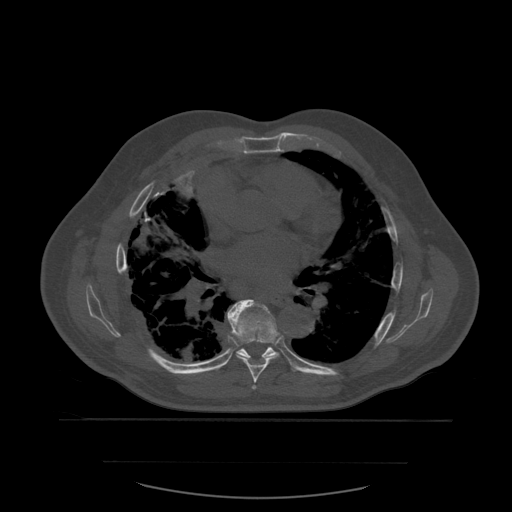
CT including the spine, one axial slice; position 376 of 590 along the scan axis; bone window (W 1800 / L 400 HU); 1.25 mm slice thickness; 512 × 512 image matrix, field of view 479 × 479 mm. Patient age 71 years. From the clinical record (not read from this slice): primary cancer: lung; vertebrae with lytic lesions (as recorded): T1, T2, L5, S1.
Outlined on this slice (semi-automatic segmentation, software-assisted and operator-edited):
- T6 vertebra: box from (x=252, y=386) to (x=257, y=390) px
- T7 vertebra: (x=228, y=299)–(x=280, y=383)
- T8 vertebra: (x=227, y=310)–(x=280, y=361)